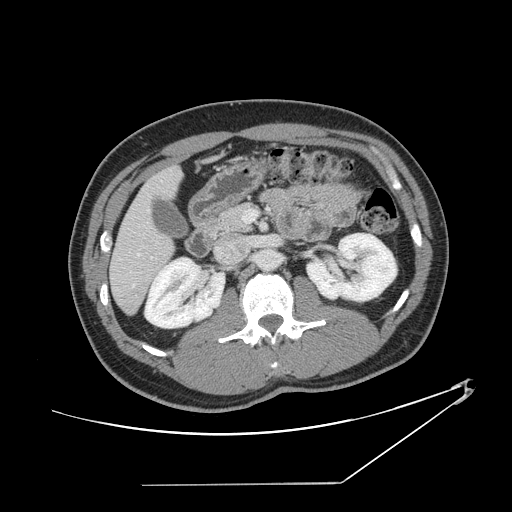
Contrast-enhanced abdominal CT, one axial slice; slice 63 of 152 in the series (ordered by position); reconstruction kernel STANDARD; intravenous contrast given; soft-tissue window (W 400 / L 40 HU); 512 × 512 image matrix, field of view 432 × 432 mm. Male patient, age 45 years. Case-level facts recorded for this patient, not image findings: diagnosis: colorectal cancer liver metastases, imaged before liver resection; multiple liver metastases: no; largest metastasis: 1 cm; disease in both lobes: no.
Structures marked on this image (outlined manually by an expert reader):
- hepatic veins: bounding box (x1, y1, x2, y2) in pixels: (137, 210, 149, 257)
- liver: (110, 169, 180, 313)
- planned liver remnant (the part of the liver to remain after resection): (111, 169, 180, 313)
- portal vein (with intrahepatic branches): (242, 210, 257, 222)